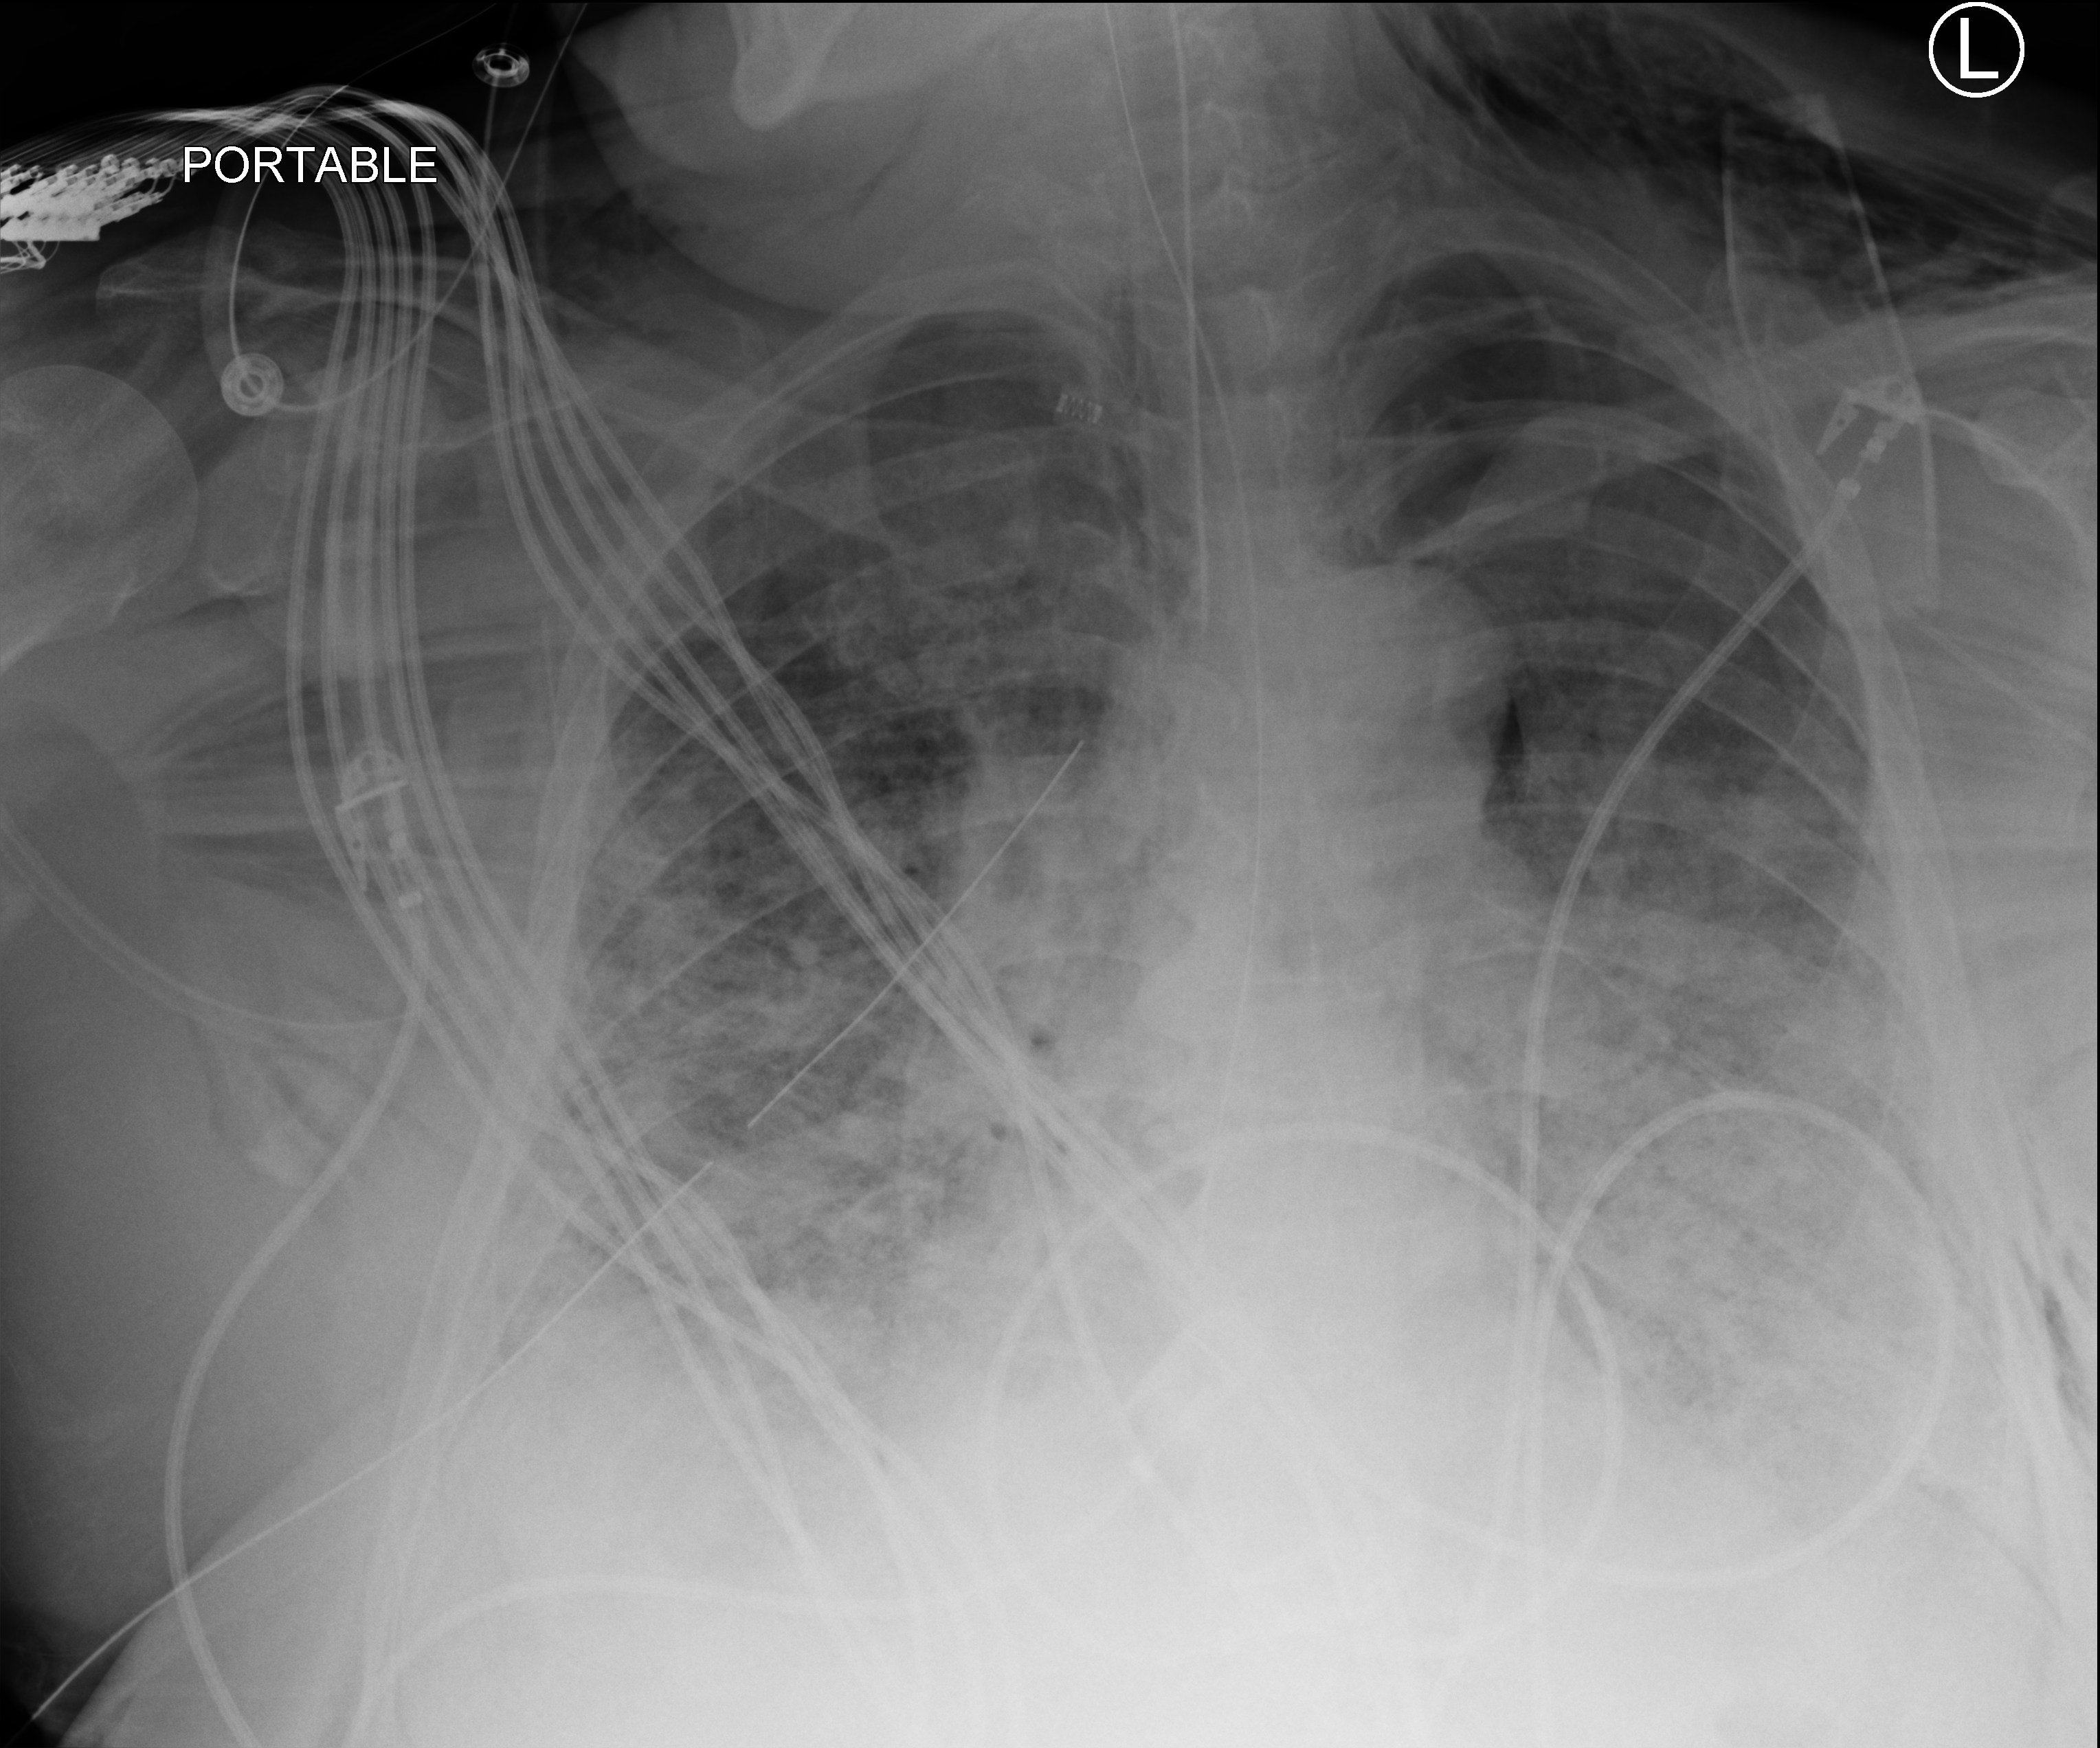
Portable chest radiograph, anteroposterior (AP) projection. Adult patient hospitalised with COVID-19, age 18–59 years.
Admission-level facts for this patient (not findings on this image; timing relative to this image not recorded):
- mechanically ventilated during this hospital stay: yes
- length of hospital stay: 28 days
- admitted to intensive care during this hospital stay: yes